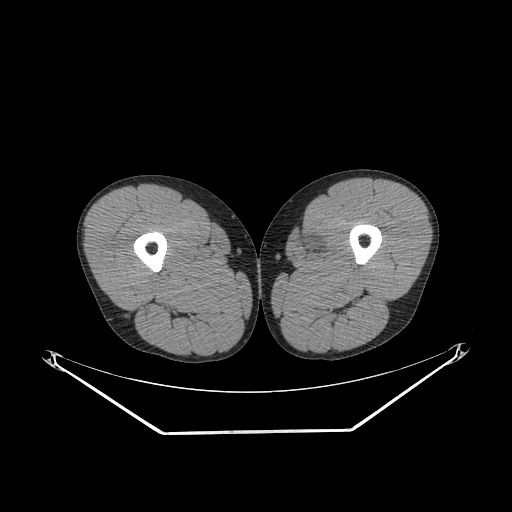
CT of an extremity soft-tissue mass (from a PET/CT study), one axial slice; position 262 of 311 along the scan axis; reconstruction kernel SOFT; 140 kVp; soft-tissue window (W 400 / L 40 HU); 3.75 mm slice thickness; 512 × 512 image matrix, field of view 500 × 500 mm. Male patient. From the clinical record (not read from this slice): histological type: mixoid liposarcoma; grade: low; site of the primary tumour: left thigh.
Annotated regions visible in this slice (expert contour drawn on MRI and transferred to this co-registered scan by the dataset authors):
- gross tumour volume (mass): bounding box (x1, y1, x2, y2) in pixels: (301, 234, 323, 255)